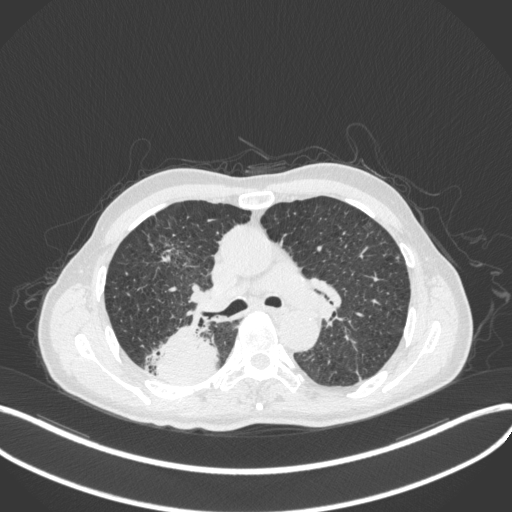
Chest CT, one axial slice. Position 288 of 423 along the scan axis. 120 kVp. Lung window (W 1500 / L -600 HU). 512 × 512 image matrix, field of view 400 × 400 mm. Male patient, age 79 years. From the clinical record (not read from this slice): clinical TNM (as recorded): T3 N0 M0.
Outlined on this slice (bounding box drawn by a radiologist):
- lung tumour (recorded histology: adenocarcinoma): box from (x=154, y=318) to (x=220, y=386) px